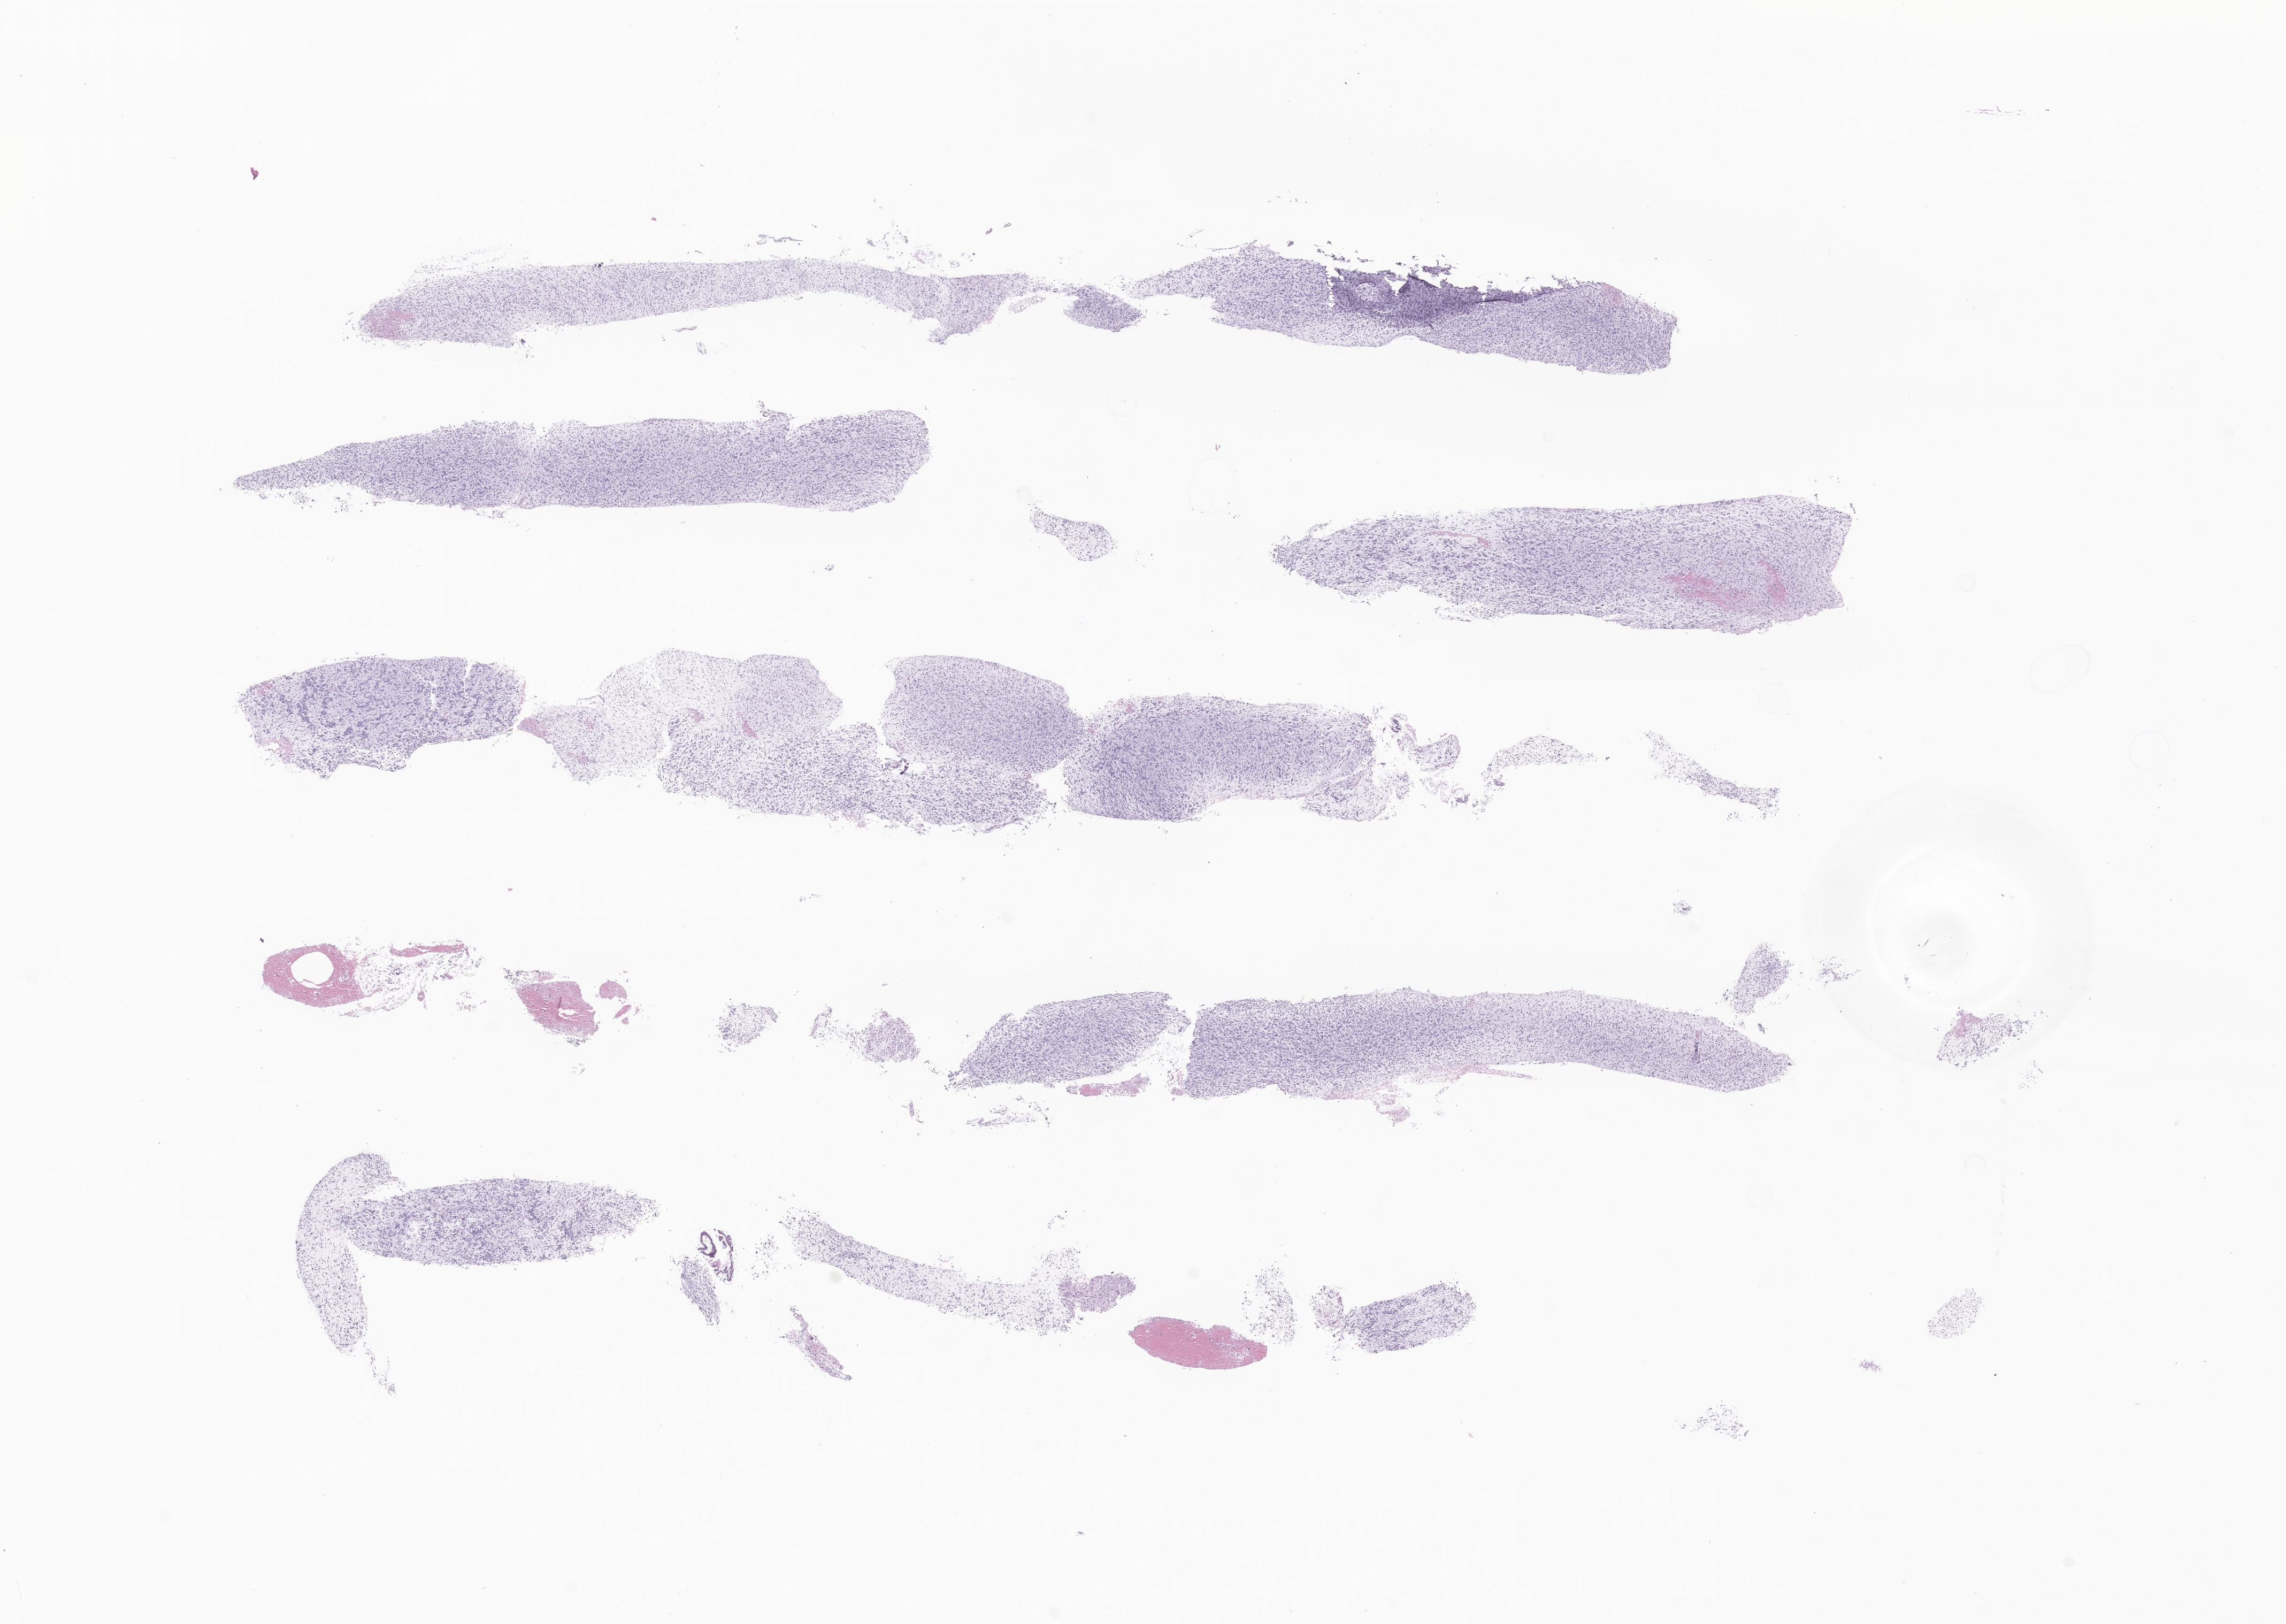
Haematoxylin and eosin whole-slide image of tumor tissue from the brain stem — whole scanned area (about 18.0 x 12.8 mm) shown as a low-resolution overview, formalin-fixed paraffin-embedded section. Male patient, age 67 months.
Diagnosis (ICD-O-3 morphology term): Glioma, malignant.